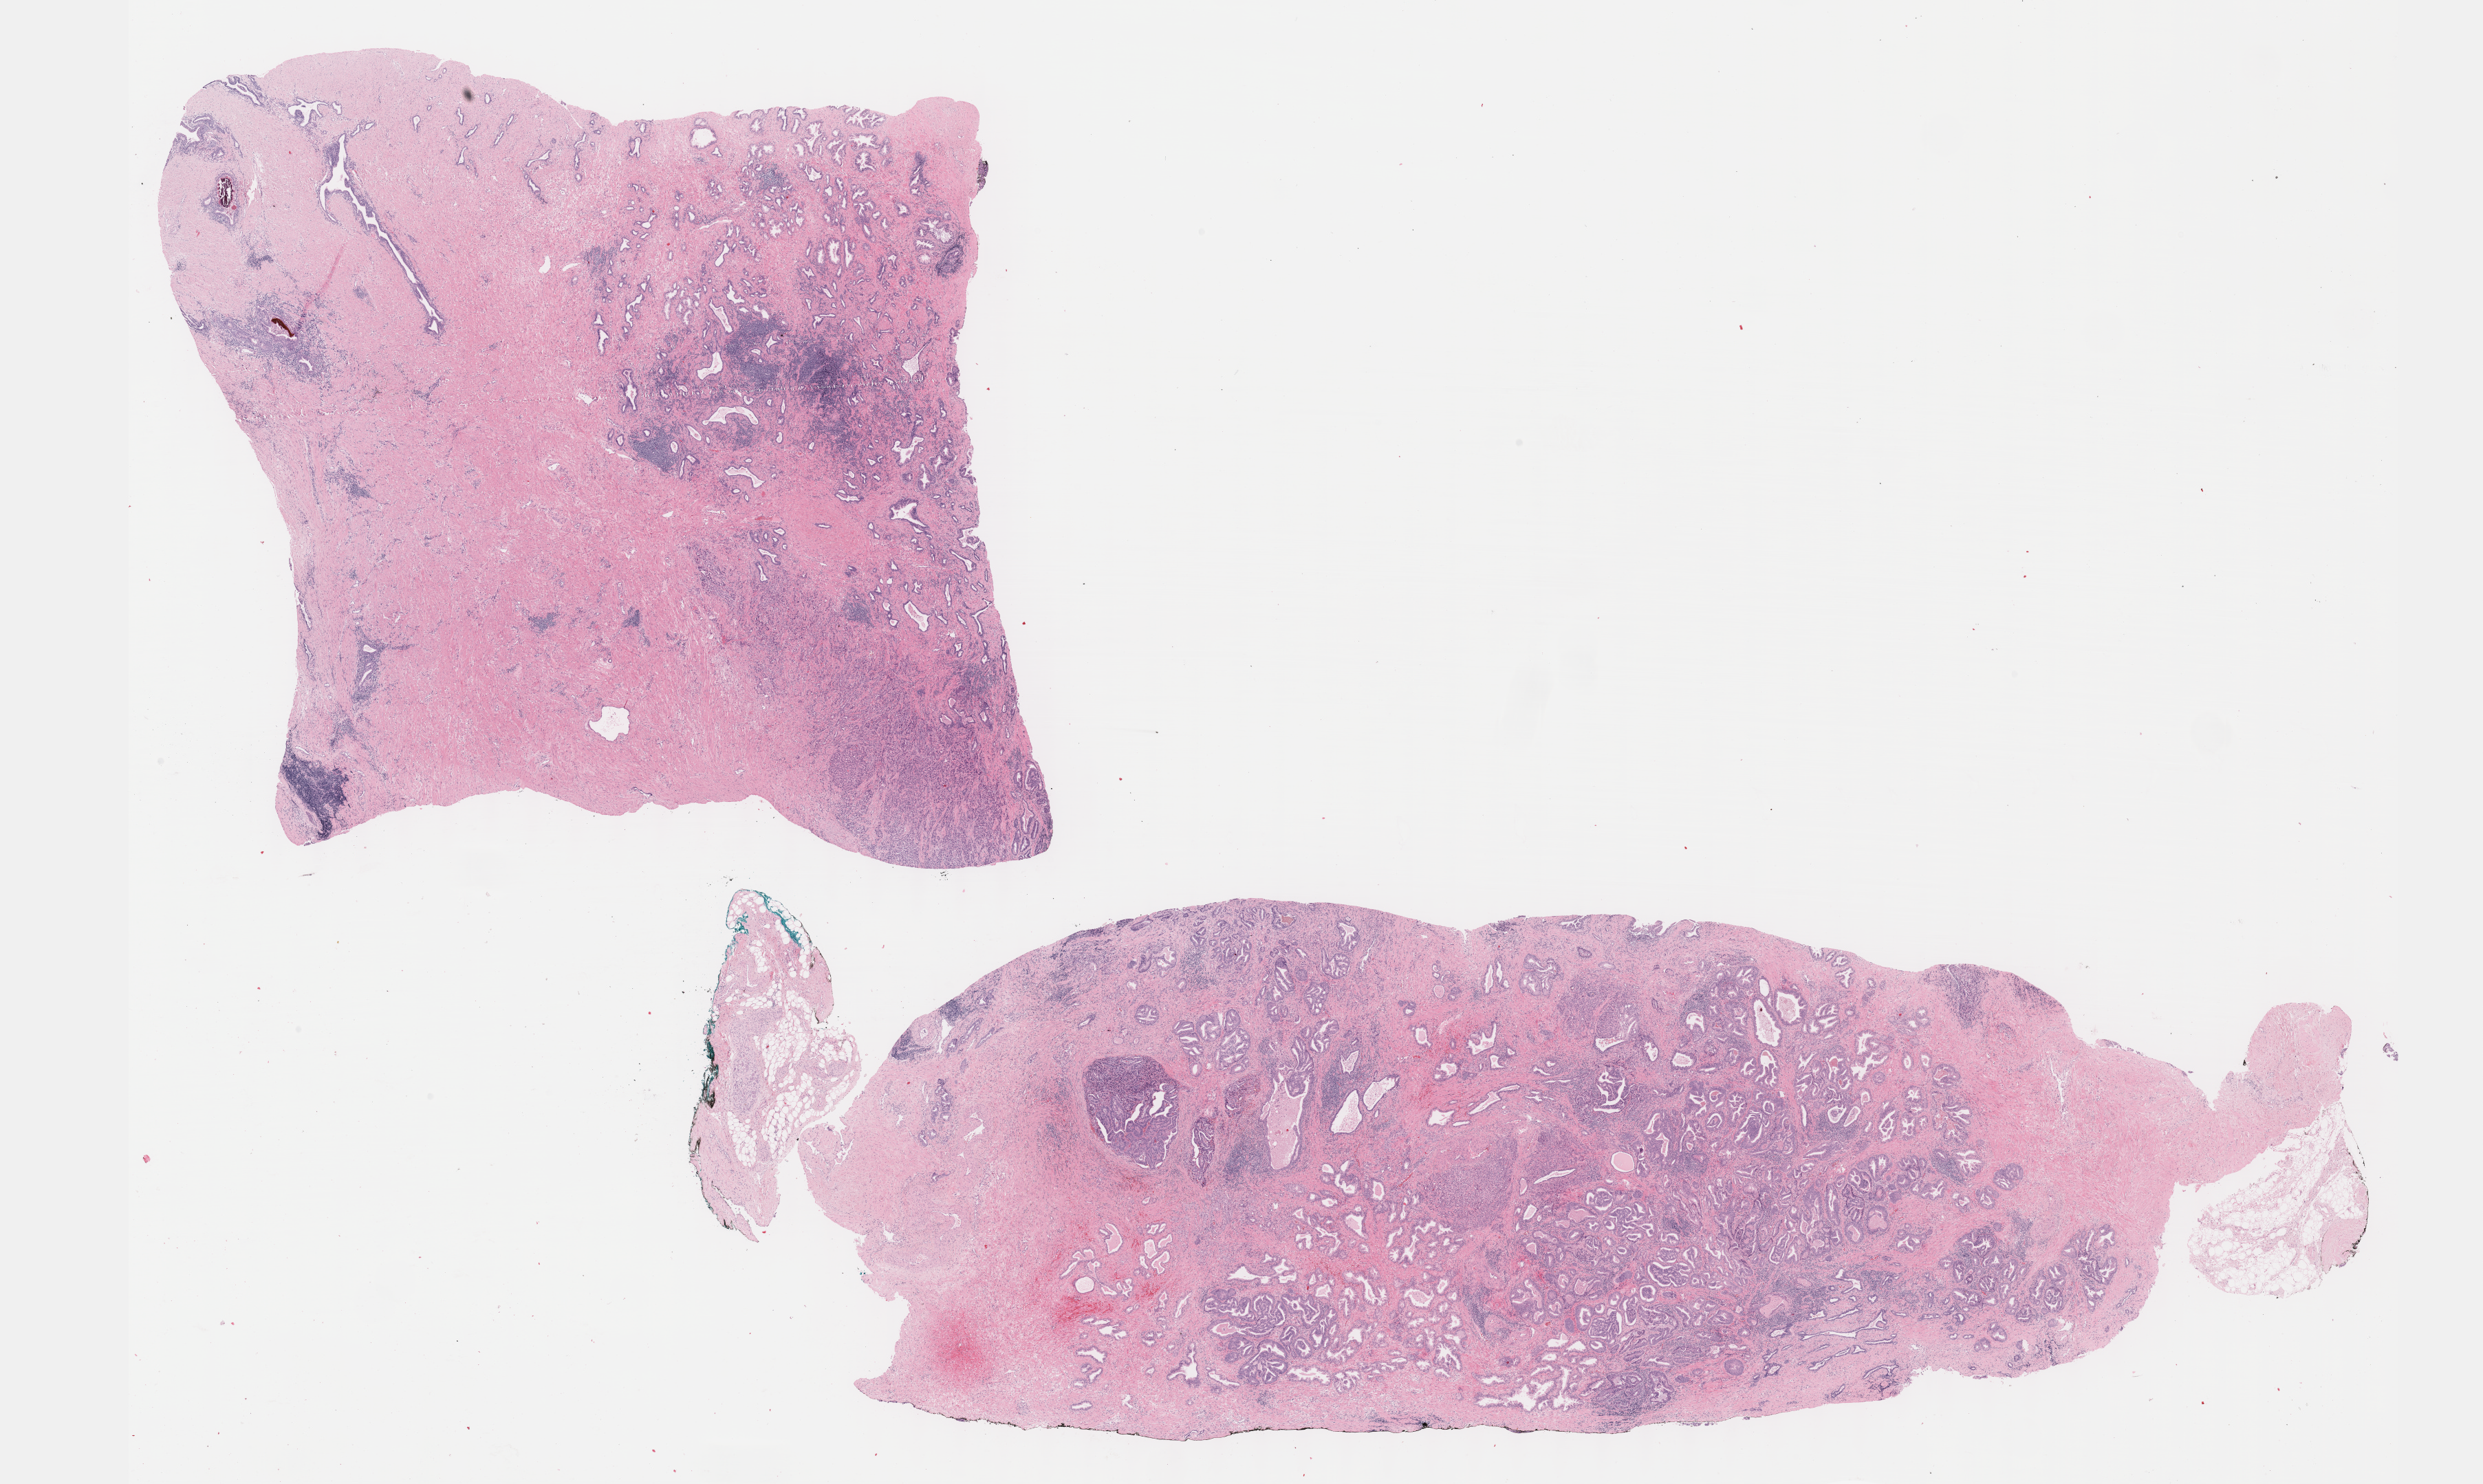
Digitized Hematoxylin and eosin (H&E) stained tissue section (whole slide), low-resolution overview of the scanned area, about 28.7 x 17.2 mm; formalin-fixed paraffin-embedded (FFPE) diagnostic section; sample: primary tumour, prostate. Patient: male, age at initial diagnosis 66 years. Gleason score: 9 (4+5).
Pathologic diagnosis: Adenocarcinoma, NOS (prostate gland). Laterality: bilateral.